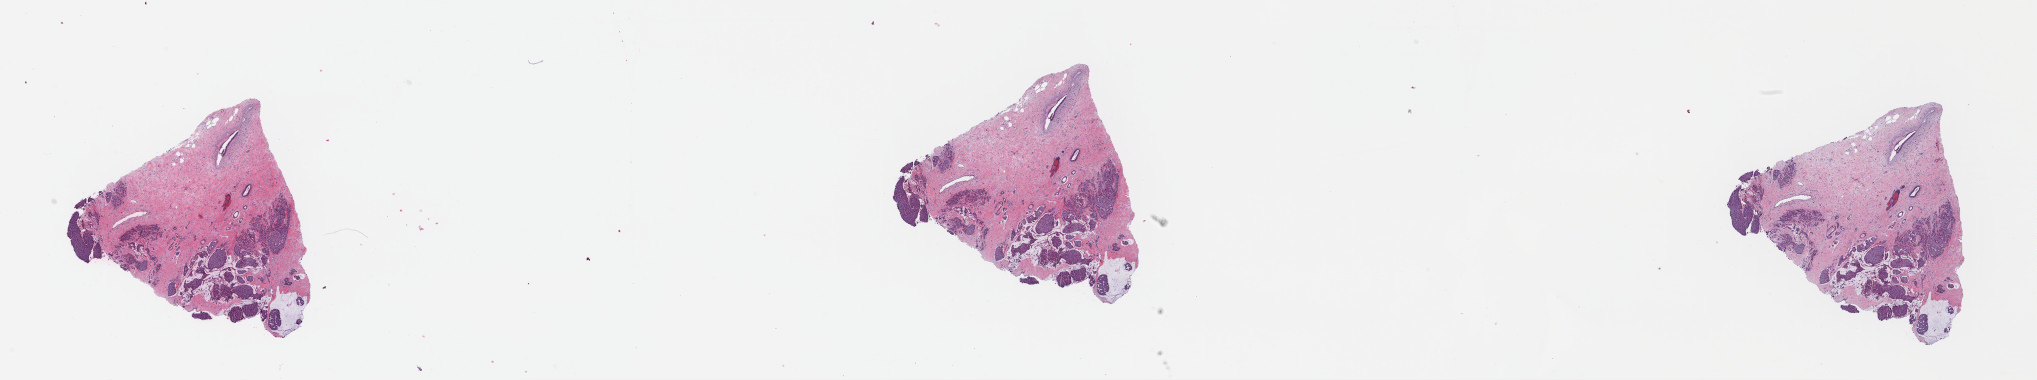
Hematoxylin and eosin (H&E) stained whole-slide image, shown as a low-resolution overview of the whole scanned area (about 32.0 x 6.0 mm, slide scanned at 40x); FFPE section; breast, primary tumour sample. Female patient; age at initial diagnosis 62 years.
Pathologic diagnosis: Mucinous adenocarcinoma.